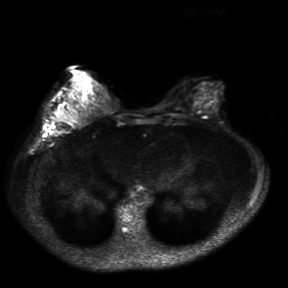
Breast MRI, one axial slice; slice 12 of 30 in the series (ordered by position); diffusion-weighted series; image 2 of 4 stored at this slice position (different b-values; order by instance number); 3 T; 4 mm slice thickness; 288 × 288 image matrix, field of view 360 × 360 mm. Female patient.
Annotated regions visible in this slice (outlined manually by an expert reader):
- tumour on diffusion-weighted imaging: box from (x=56, y=109) to (x=67, y=123) px